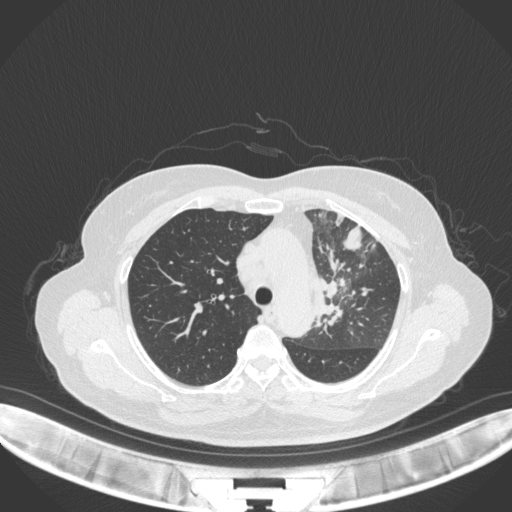
Chest CT, one axial slice; position 245 of 382 along the scan axis; reconstruction kernel B31f; 120 kVp; lung window (W 1500 / L -600 HU); 1 mm slice thickness; 512 × 512 image matrix, field of view 400 × 400 mm. Female patient, age 64 years. From the clinical record (not read from this slice): clinical TNM (as recorded): T2a N2 M0.
Annotated regions visible in this slice (rectangle marked by the reading radiologist):
- lung tumour (recorded histology: adenocarcinoma): bounding box (x1, y1, x2, y2) in pixels: (310, 260, 355, 333)
- lung tumour (recorded histology: adenocarcinoma): (341, 218, 367, 250)